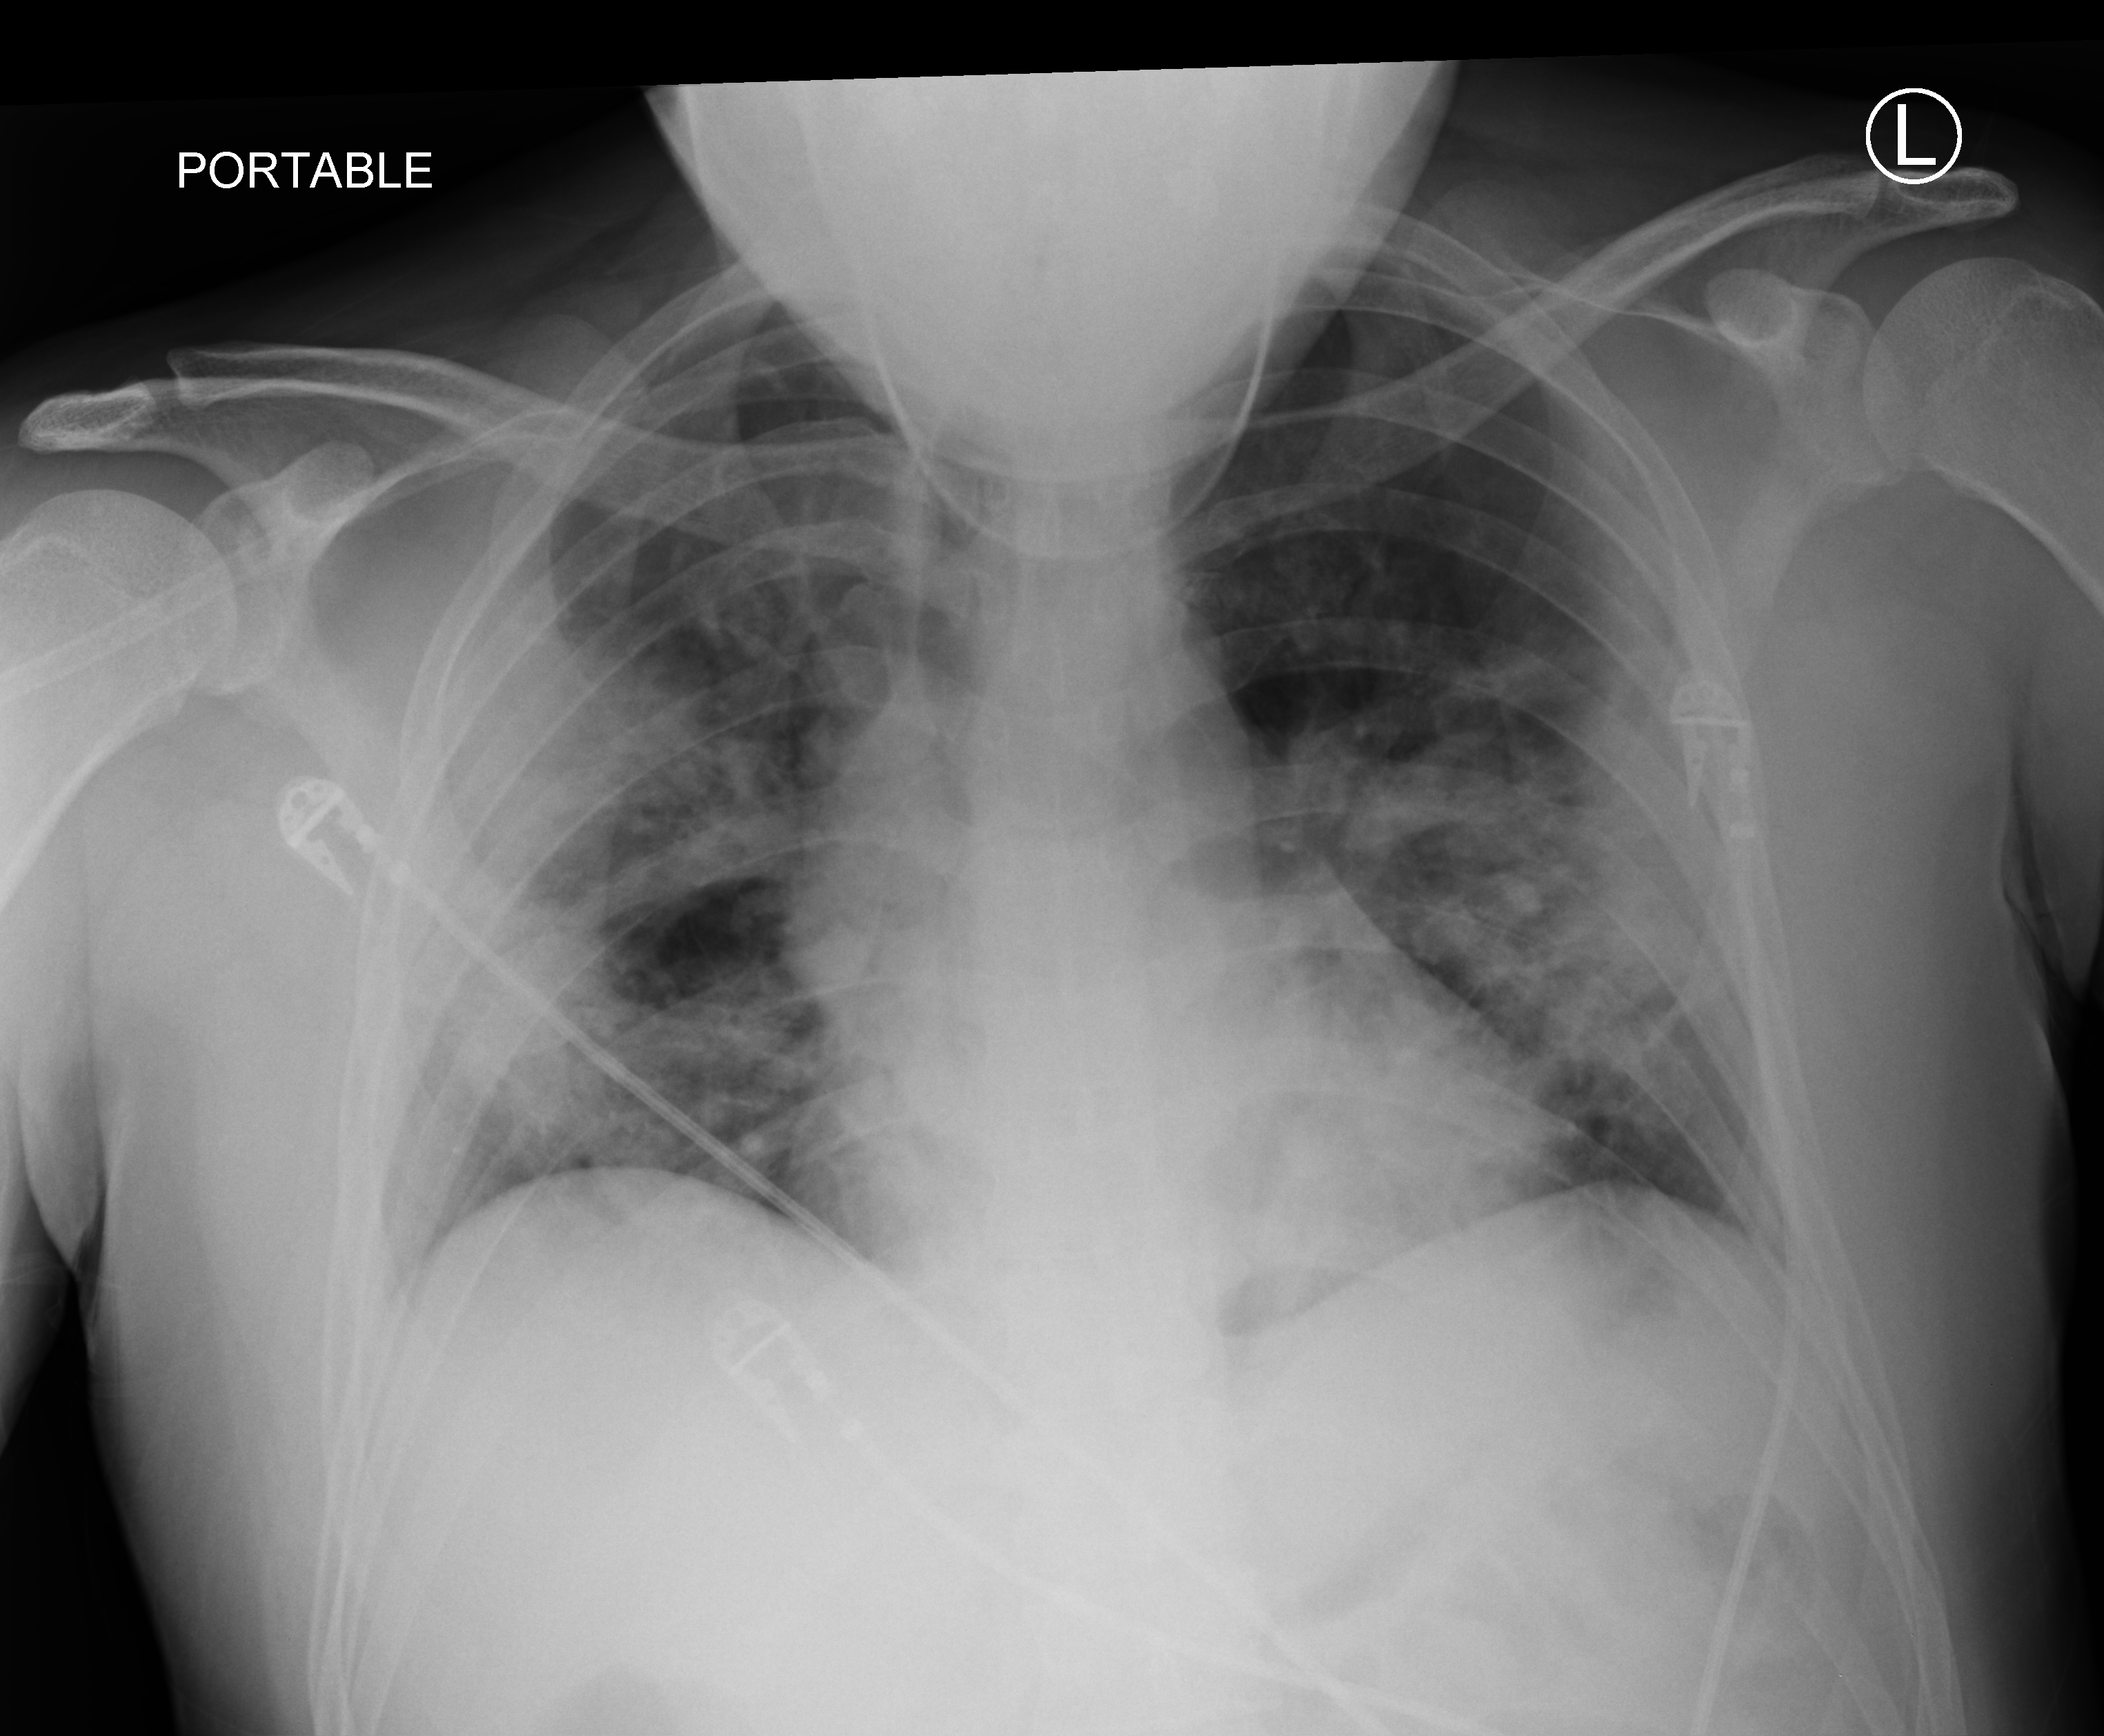
Portable chest radiograph, anteroposterior (AP) projection. Patient hospitalised with COVID-19; male, aged 18–59 years.
Admission-level facts for this patient (not findings on this image; timing relative to this image not recorded): COPD (admission record): no; admitted to intensive care during this hospital stay: no.